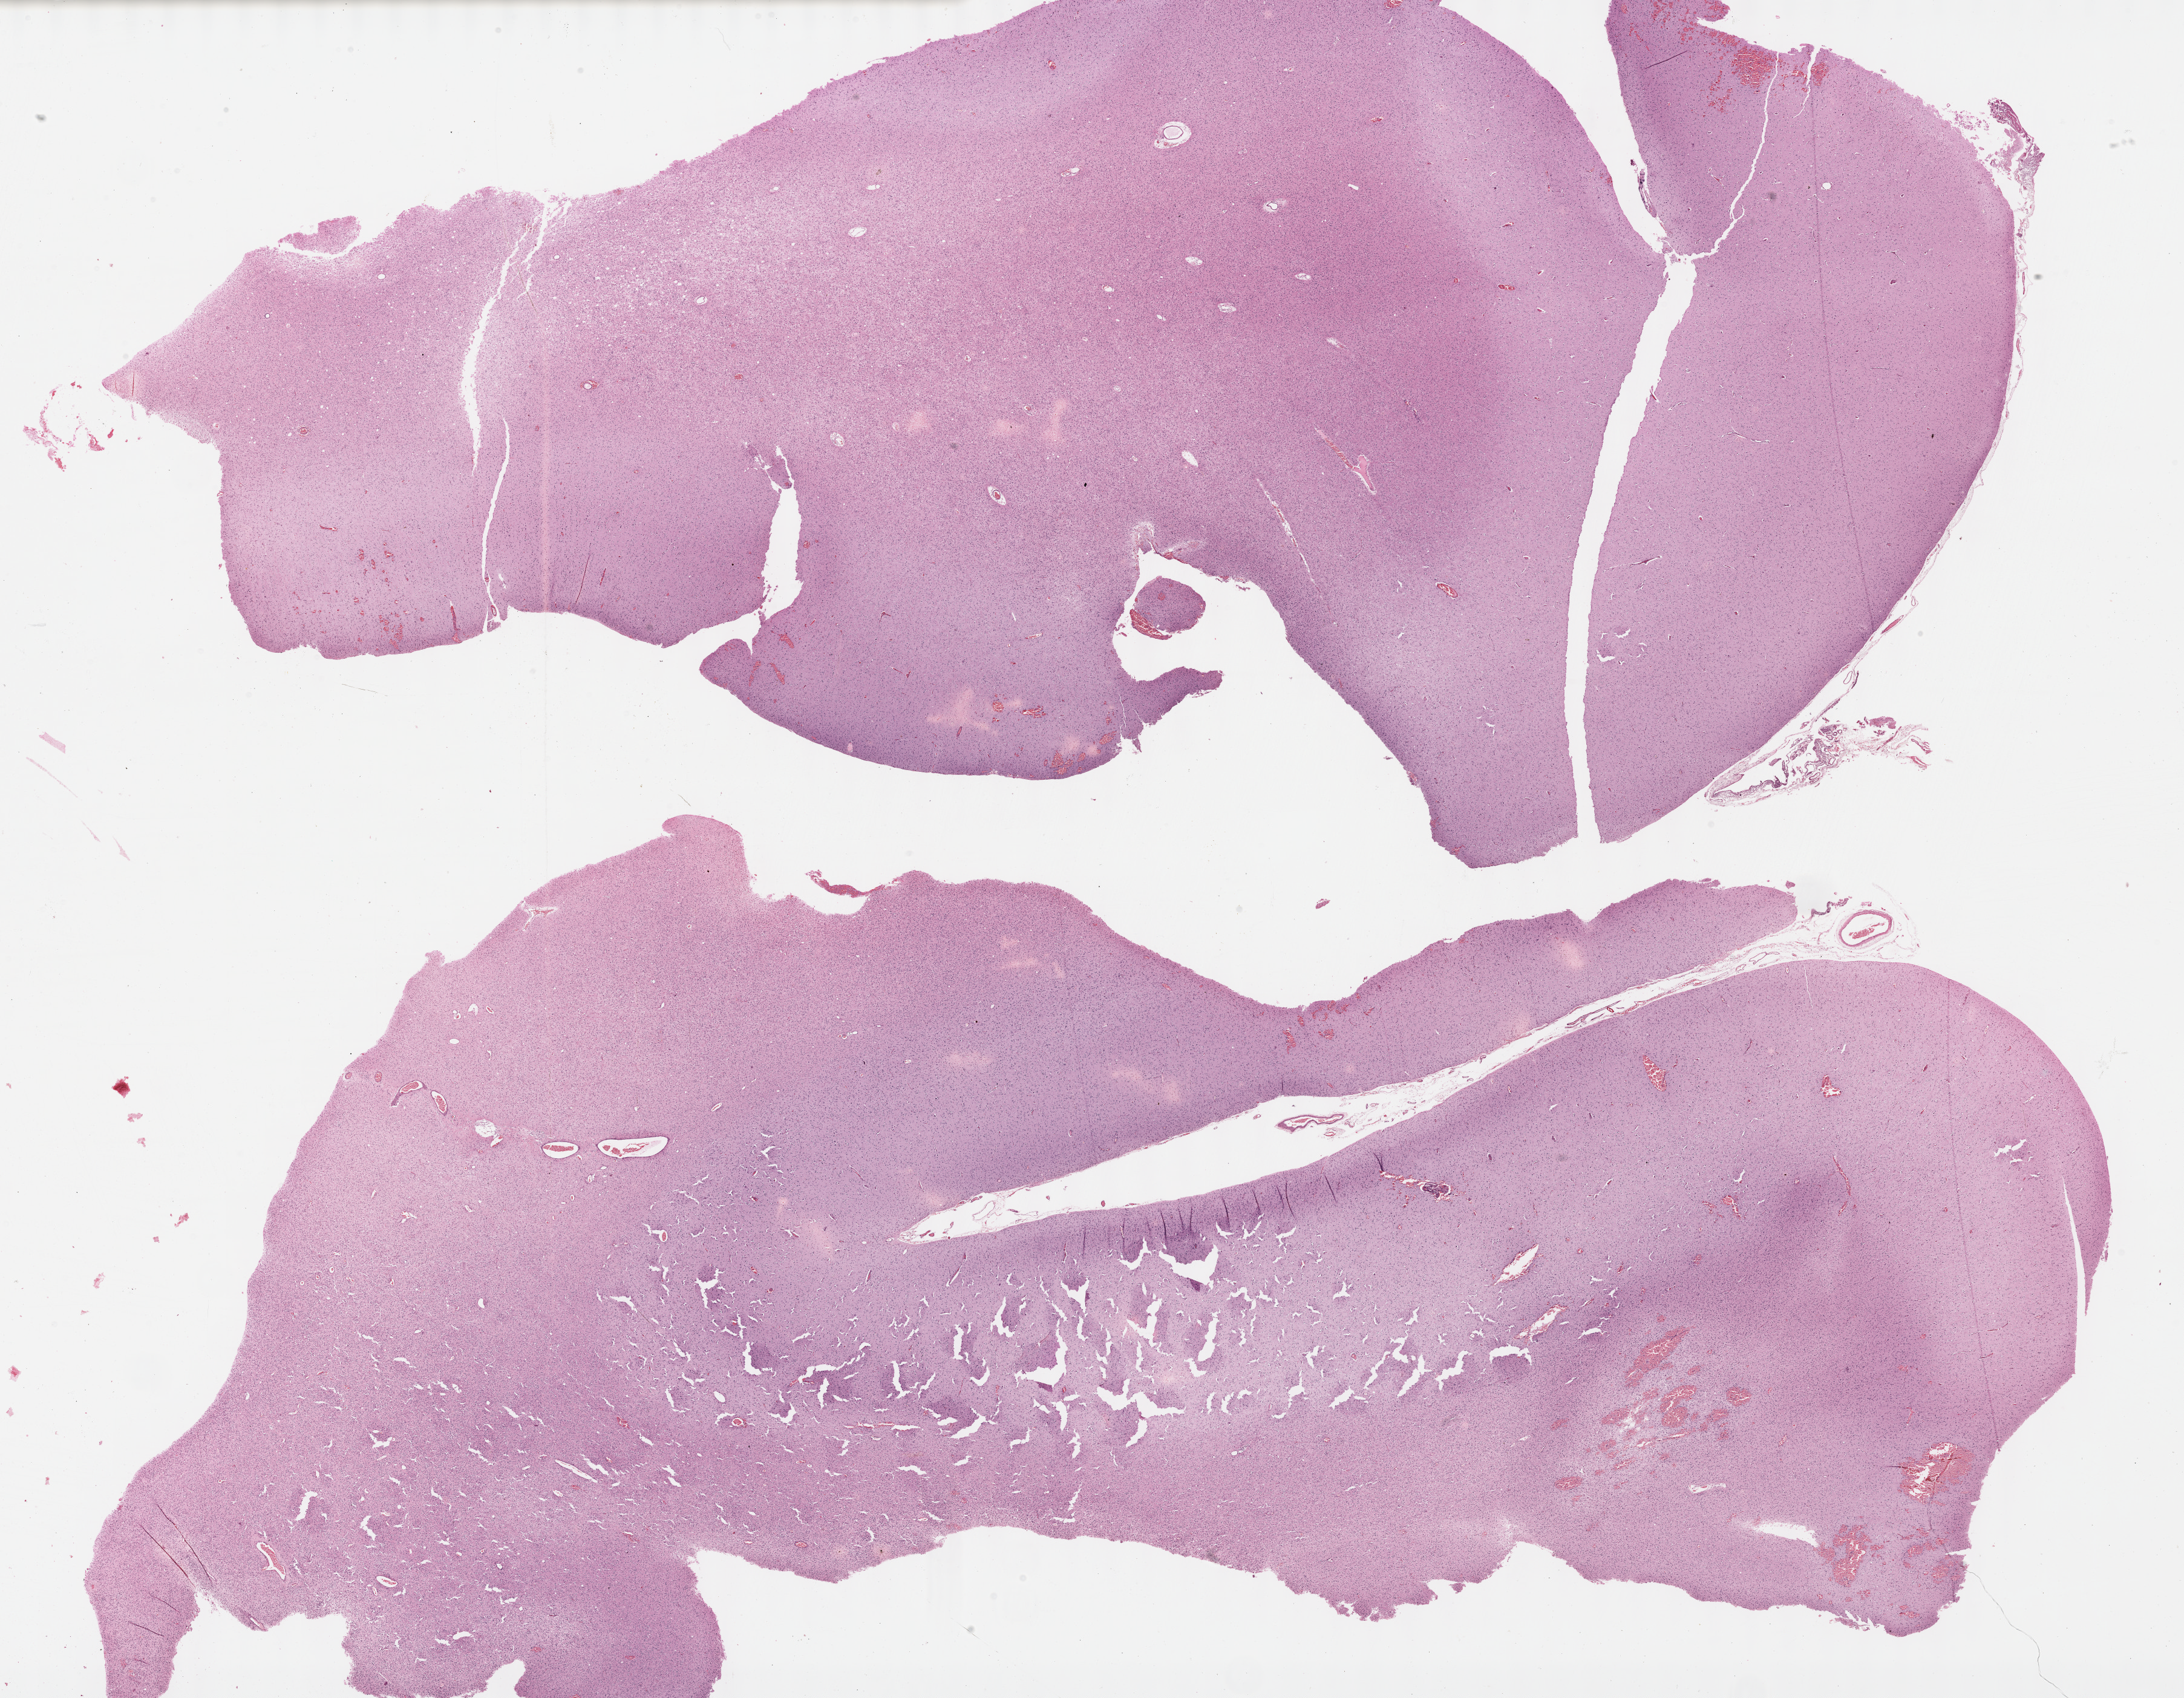
Digitized H&E-stained tissue section (whole slide) — shown as a low-resolution overview of the whole scanned area (about 29.2 x 22.7 mm). Formalin-fixed paraffin-embedded (FFPE) diagnostic section. Sample: primary tumour, brain. Male, age 38 years at initial diagnosis. Histologic grade: G2 (moderately differentiated).
Pathologic diagnosis: Mixed glioma (cerebrum).